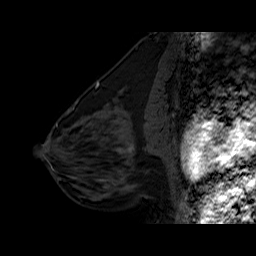
Breast MRI (dynamic contrast-enhanced), one sagittal slice. Slice 27 of 60 in the series (ordered by position). Dynamic contrast-enhanced series, time point 2 of 6 at this slice position (early post-contrast). 1.5 T. TE 6.3 ms, TR 32.5 ms. 4 mm slice thickness. 256 × 256 image matrix, field of view 200 × 200 mm. Female patient. Case-level facts recorded for this patient, not image findings: setting: breast cancer imaged before/during neoadjuvant chemotherapy; receptor status: triple-negative.
Annotated regions visible in this slice (semi-automatic segmentation, software-assisted and operator-edited):
- analysis volume of interest (the breast-tissue region the enhancement analysis was run in; not a lesion): bounding box [x1, y1, x2, y2] px = [102, 127, 162, 186]
- tumour enhancement mask (voxels above the 100 % enhancement threshold inside the analysis volume of interest): [117, 143, 134, 152]